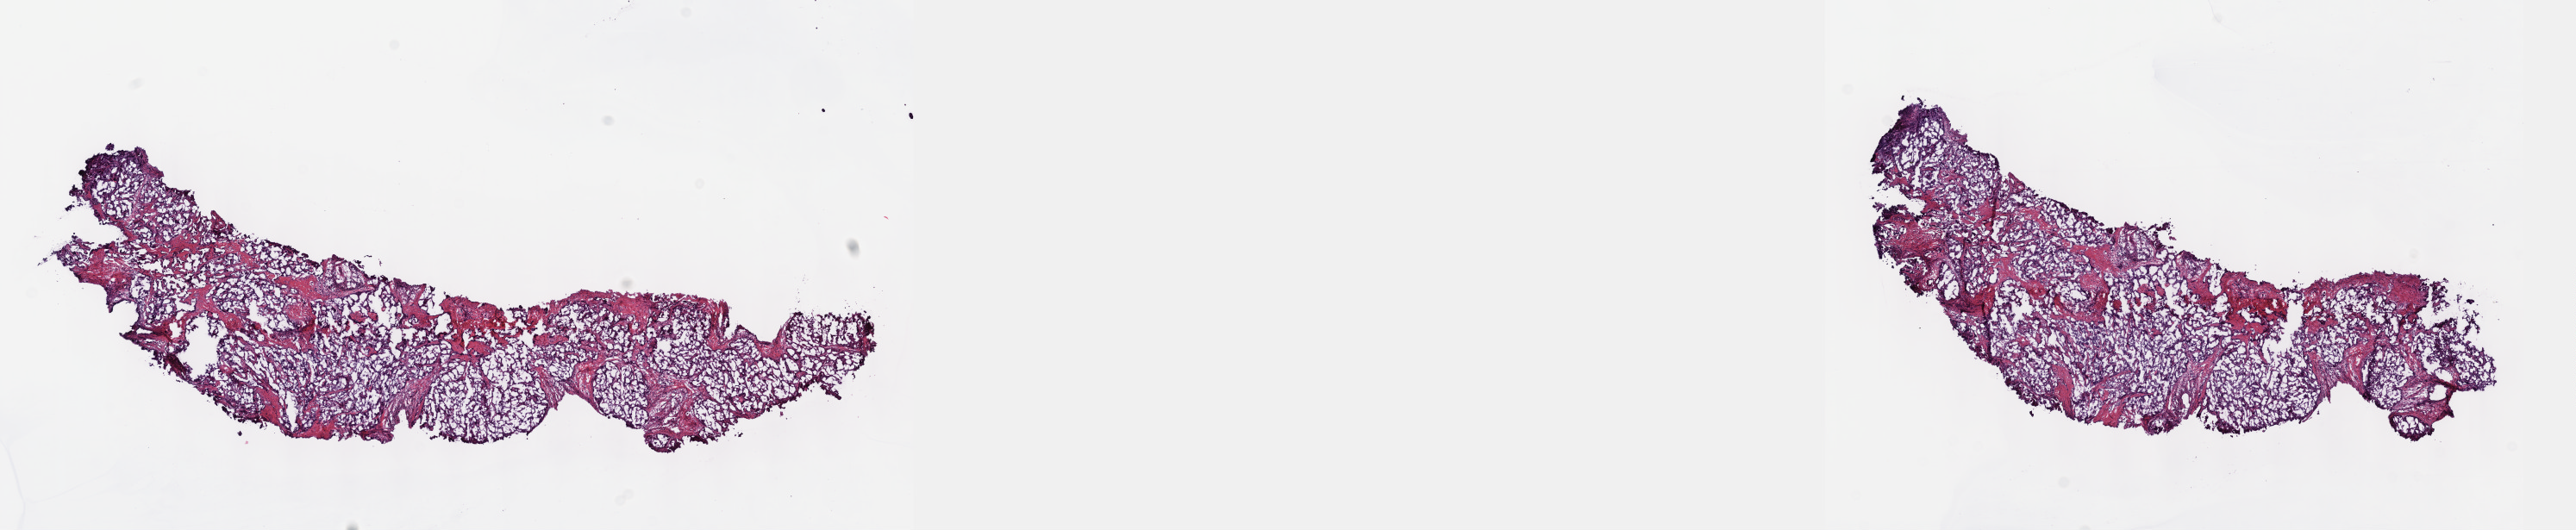
Whole-slide histology image, Hematoxylin and eosin (H&E) stained, shown as a low-resolution overview of the whole scanned area (about 24.1 x 5.0 mm, slide scanned at 40x); frozen section from the top of the tissue portion; sample: primary tumour, bile duct. Patient: male, age at initial diagnosis 60 years. Histologic grade: G2 (moderately differentiated). Composition of this section per pathologist review: tumour cells 75%, tumour nuclei 75%, normal cells 0%, stromal cells 25%, necrosis 0%. Infiltration values recorded for this section: lymphocyte infiltration 3%, monocyte infiltration 1%, neutrophil infiltration 4%.
- diagnosis: Cholangiocarcinoma
- AJCC pathologic stage: II